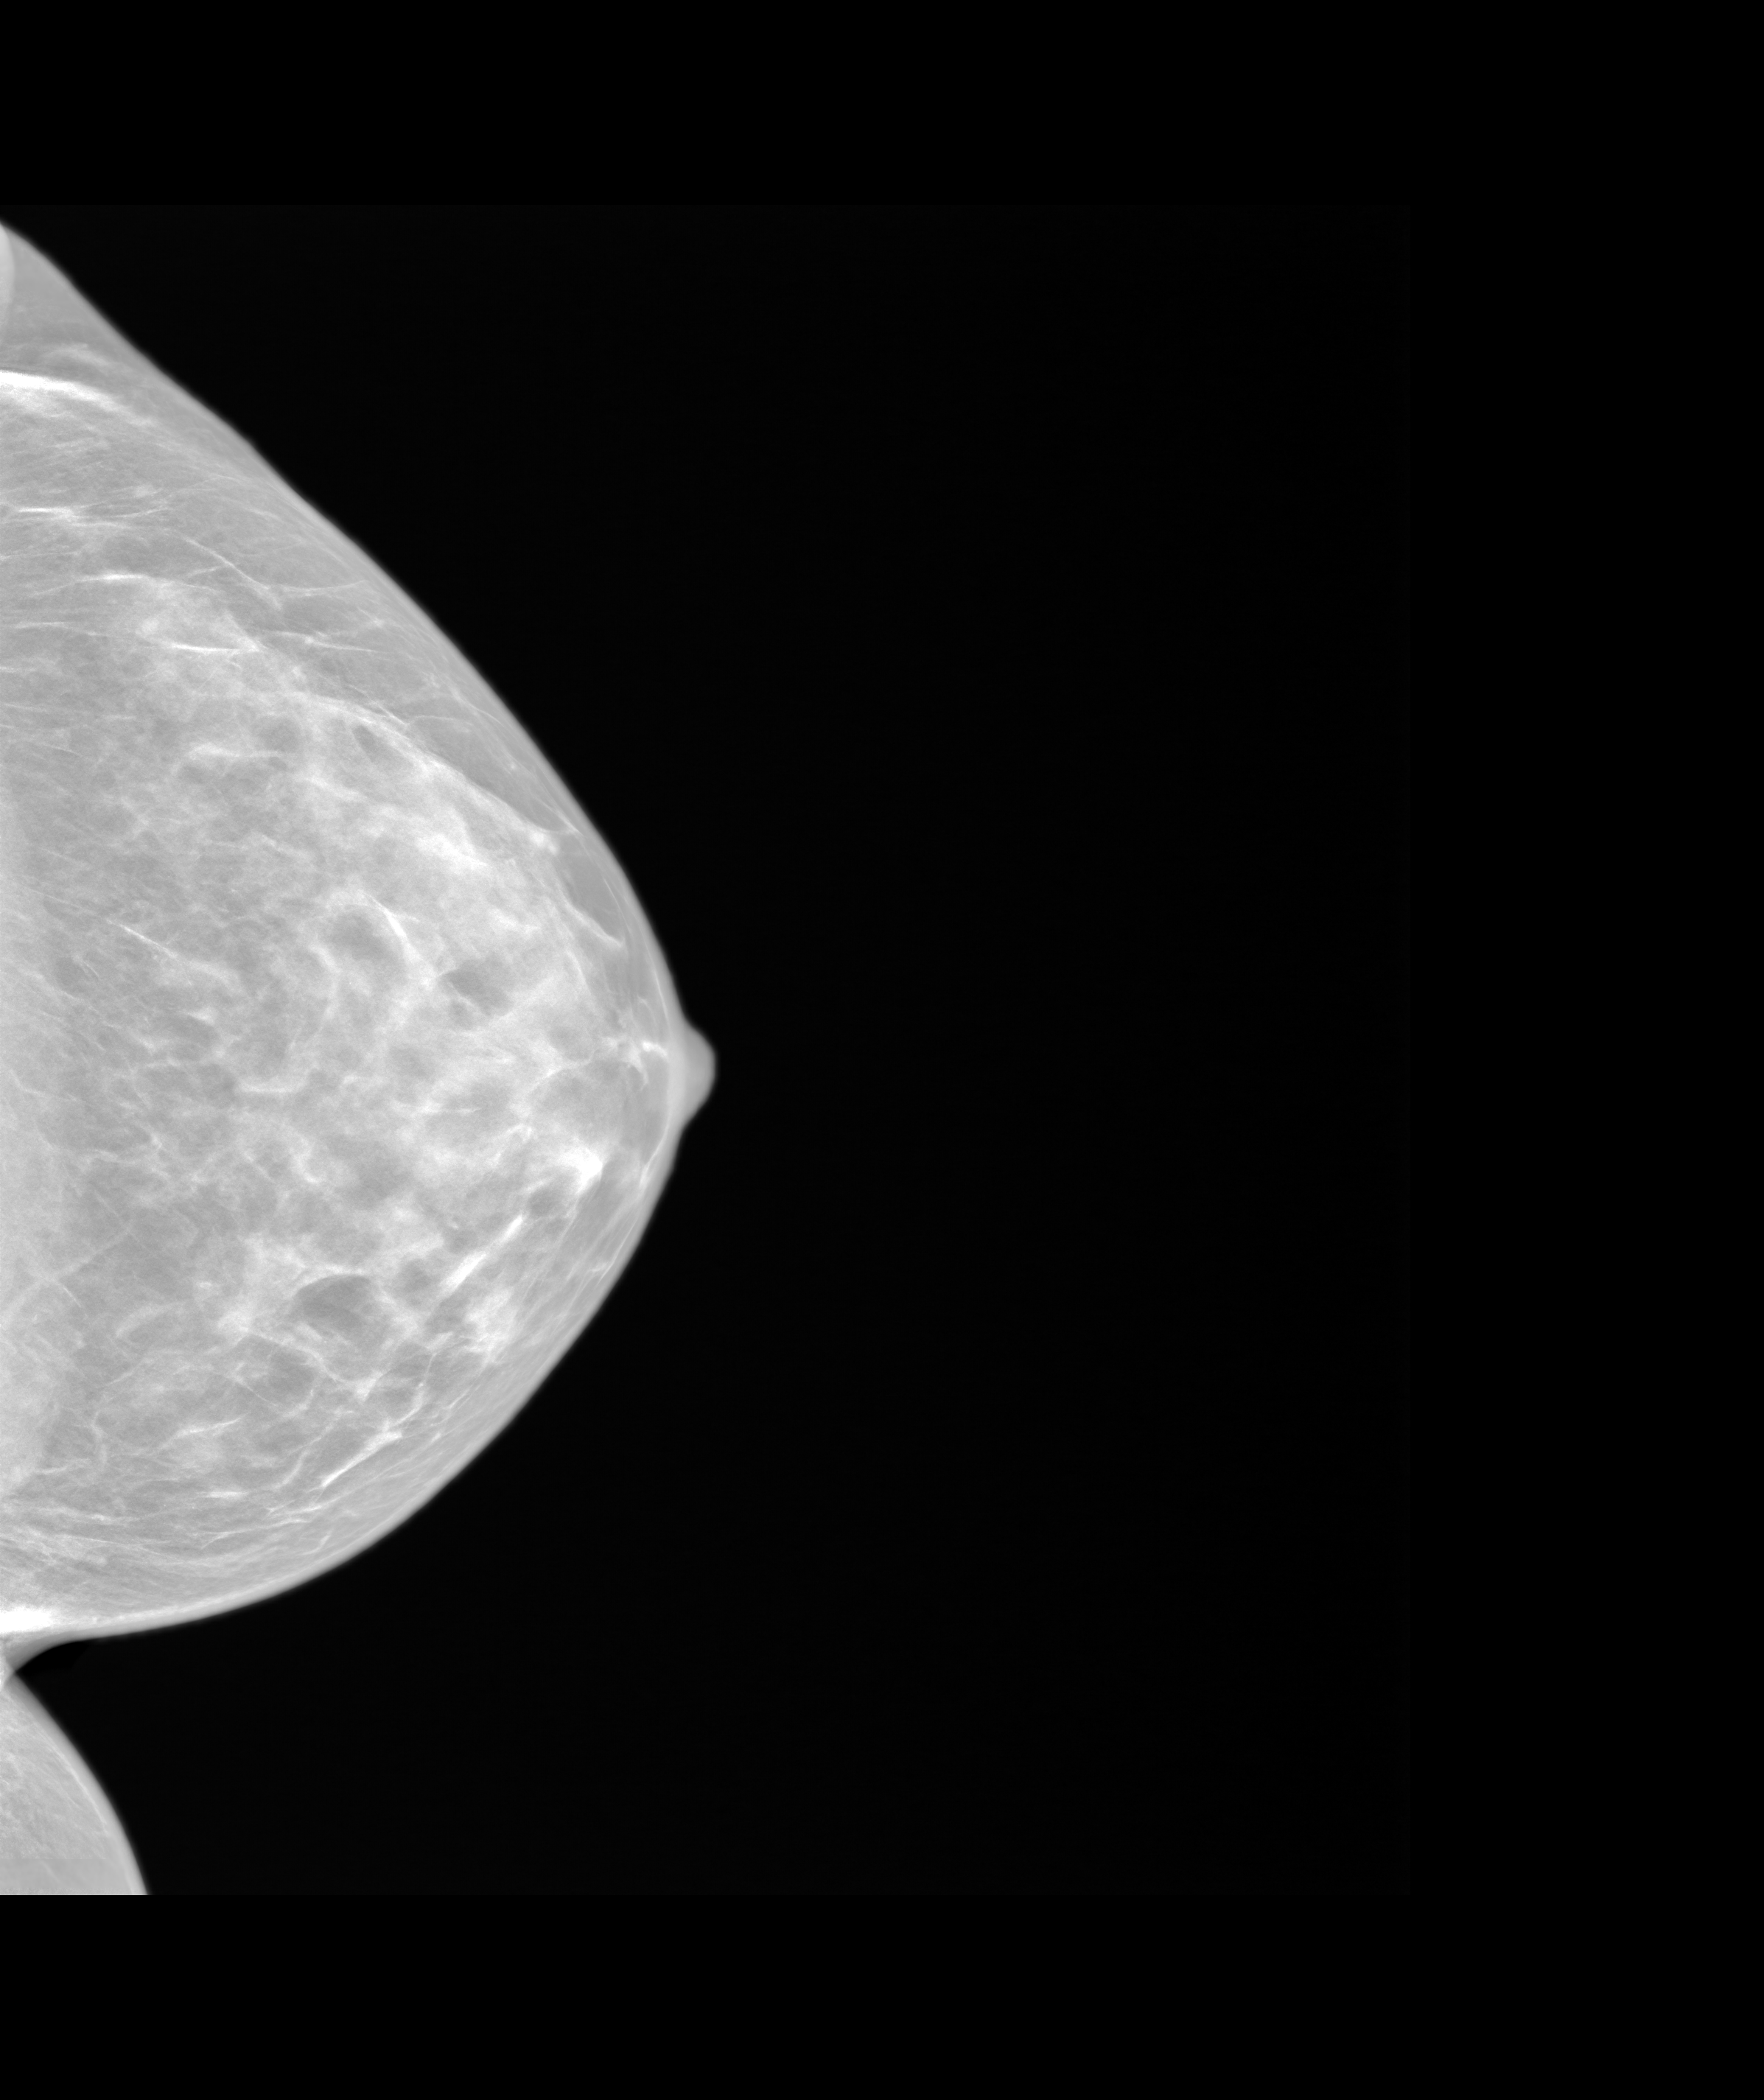
Screening examination. Patient aged 43 years (female).
Image type: synthesized 2-D view from tomosynthesis. Breast: left. Projection: cranio-caudal projection.